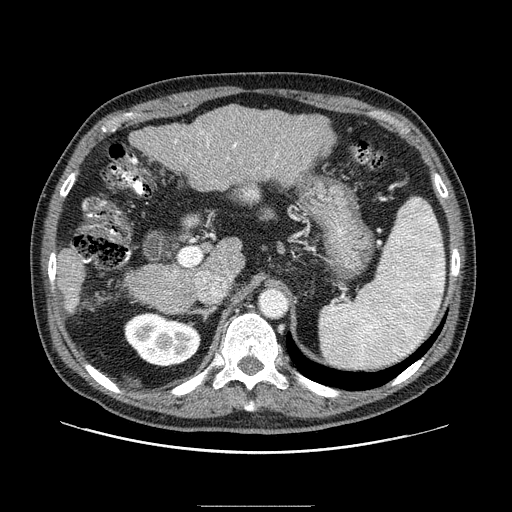
Contrast-enhanced abdominal CT (liver protocol), one axial slice. Reconstruction kernel STANDARD. One of 2 acquisitions stored at this slice position. Soft-tissue window (W 400 / L 40 HU). 512 × 512 image matrix, field of view 400 × 400 mm. Case-level facts recorded for this patient, not image findings: diagnosis: hepatocellular carcinoma (patient treated with transarterial chemoembolisation; whether this scan precedes or follows treatment is not stated here); TNM stage (as recorded): Stage-II; Child-Pugh class: A; tumour nodularity: multinodular.
Structures marked on this image (semi-automatic segmentation, software-assisted and operator-edited):
- liver parenchyma outside the tumour (the mass and vessels are separate outlines, so this box may not span the whole liver): bounding box <56,104,334,314> (left, top, right, bottom; pixels)
- liver vessels: <69,132,278,308>